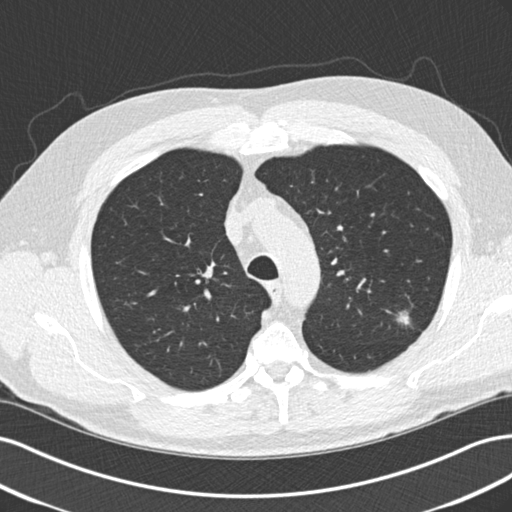
Low-dose screening chest CT, one axial slice; reconstruction kernel B30f; lung window (W 1500 / L -600 HU); 2 mm slice thickness; 512 × 512 image matrix.
Structures marked on this image (outlined manually by an expert reader):
- lesion 1 (tumor, upper lobe of left lung): bounding box <398,311,410,325> (left, top, right, bottom; pixels)